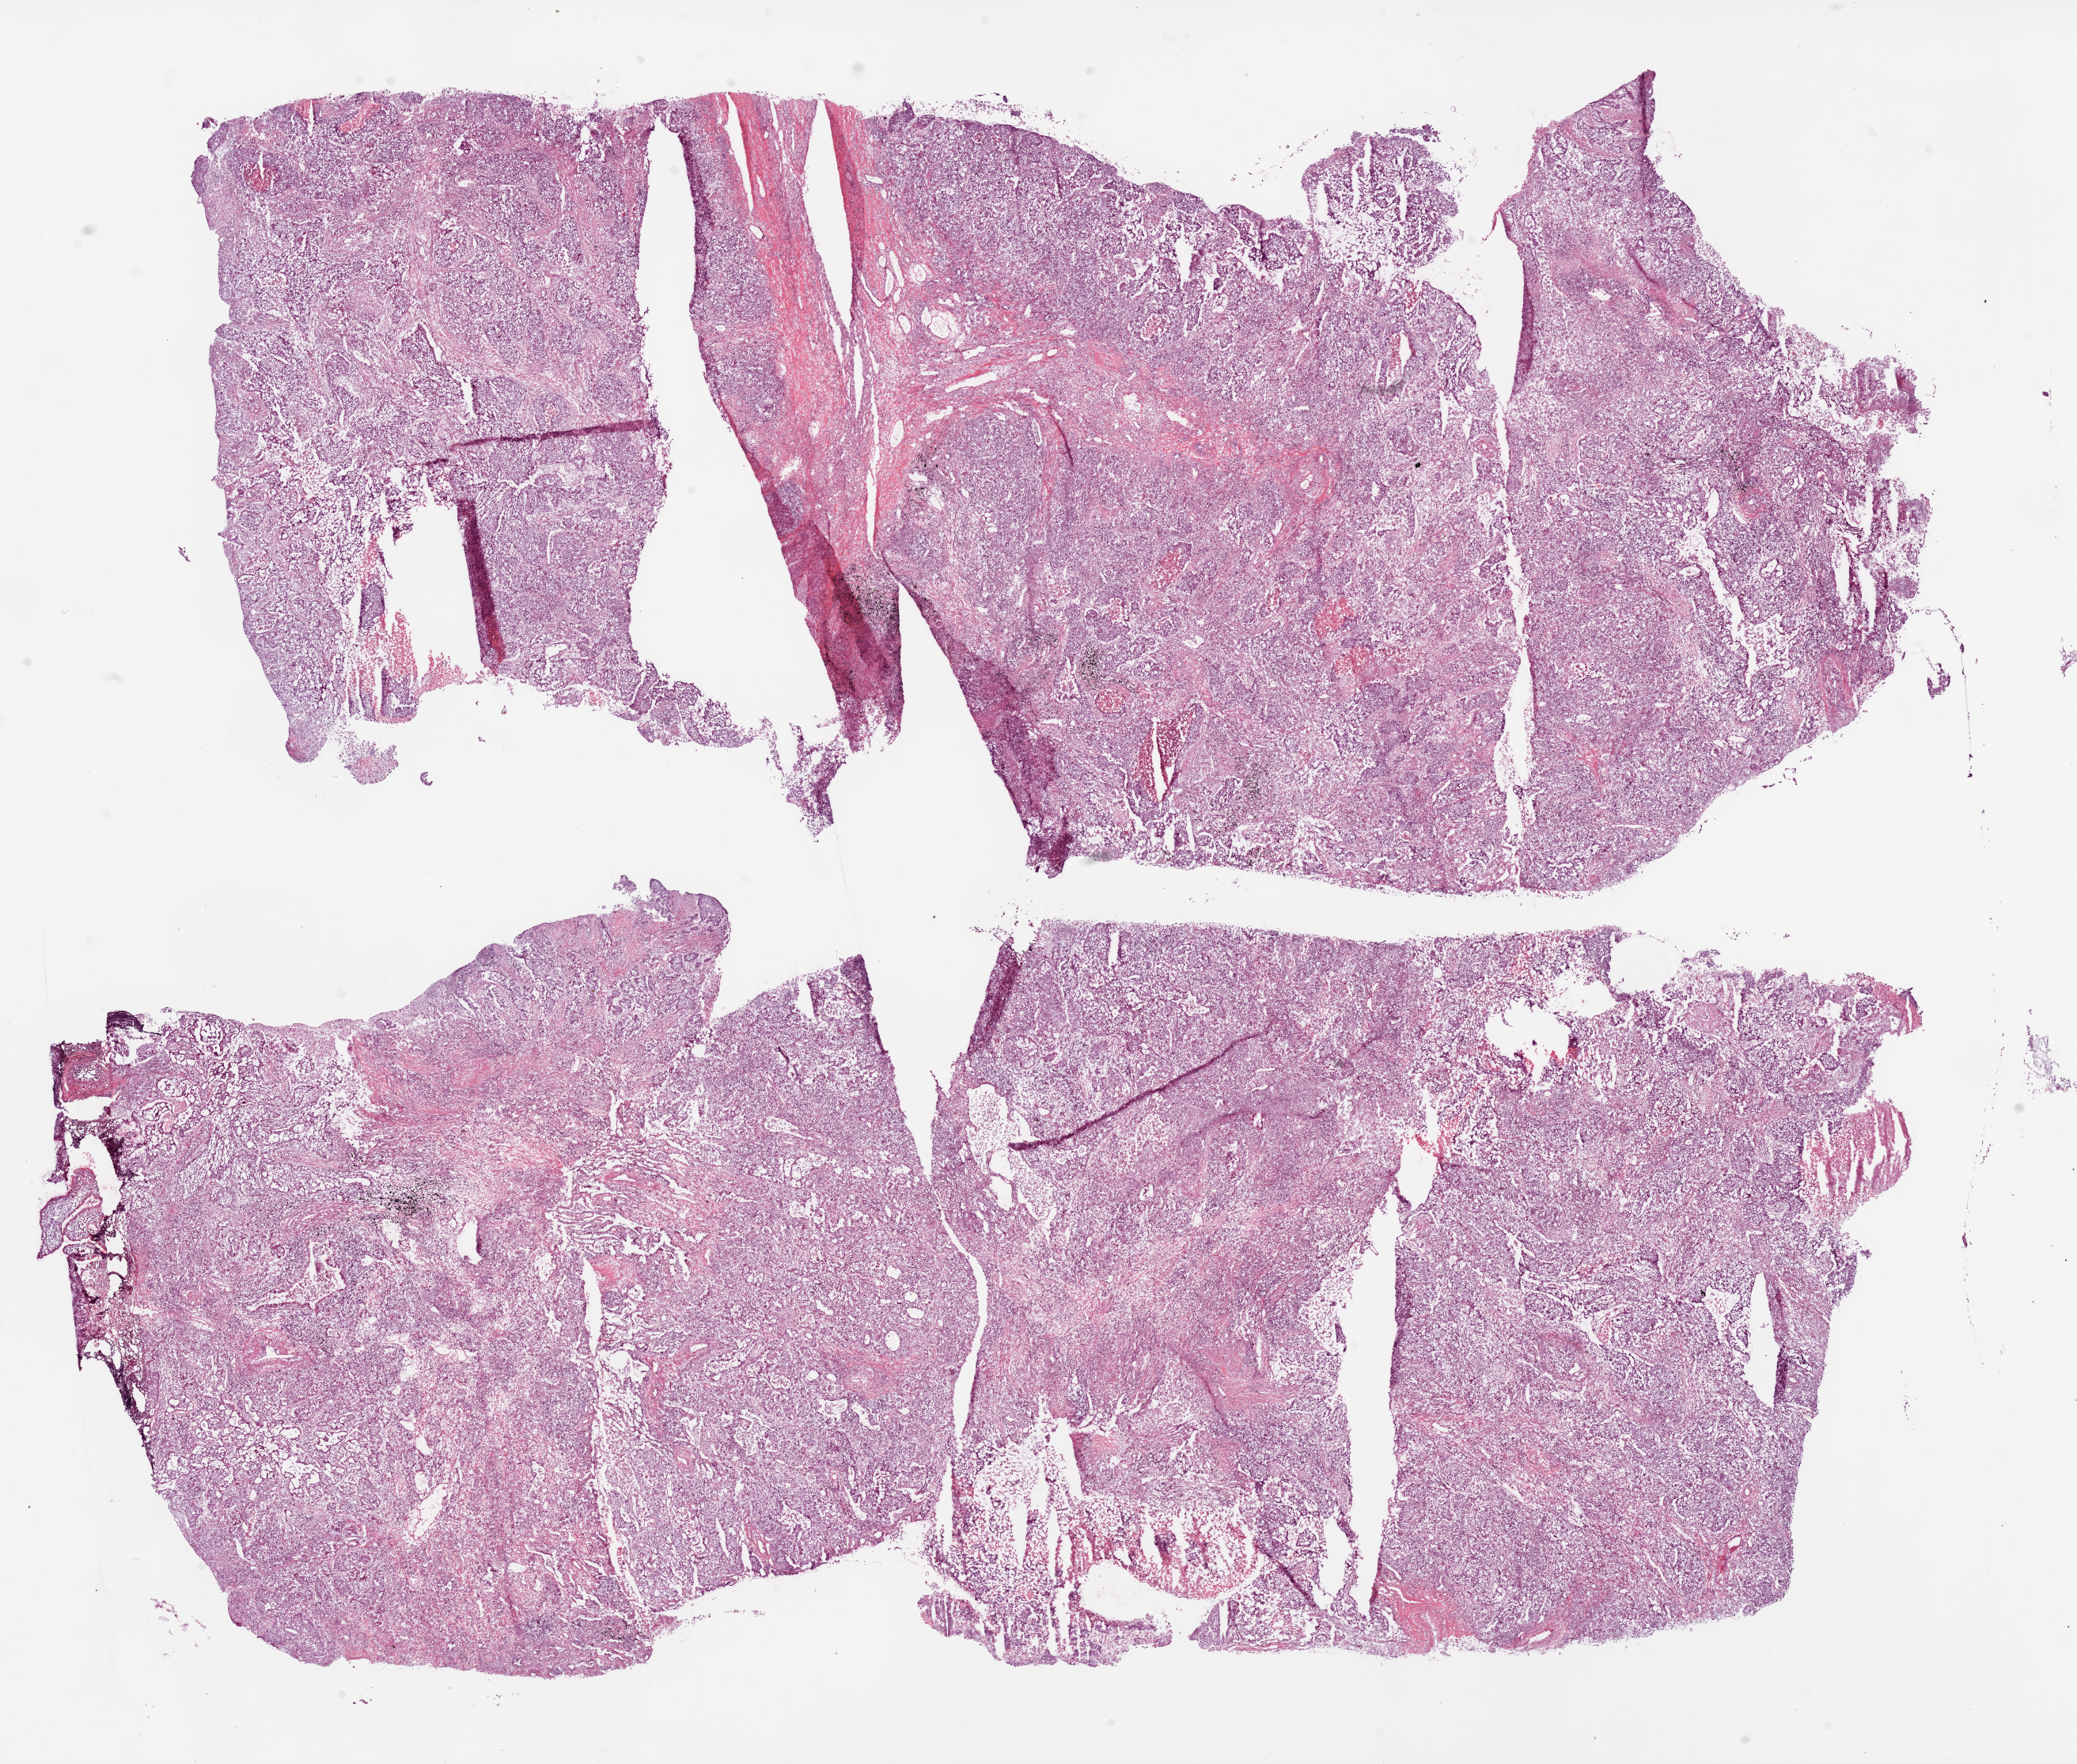
H&E whole-slide image, low-resolution overview of the scanned area, about 21.1 x 17.9 mm. Frozen section from the bottom of the tissue portion. Lung, primary tumour sample. Male, age 70 years at initial diagnosis. Pathologist review of this section (percent, as recorded): tumour cells 85%, tumour nuclei 70%, normal cells 0%, stromal cells 10%, necrosis 5%. Infiltration values recorded for this section: lymphocyte infiltration 20%, monocyte infiltration 2%, neutrophil infiltration 2%.
* AJCC pathologic stage: IB
* laterality: left
* pathologic diagnosis: Squamous cell carcinoma, NOS